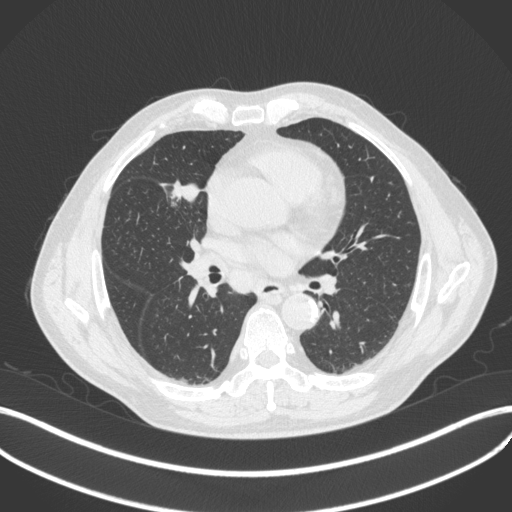
Chest CT, one axial slice; slice 204 of 429 in the series (ordered by position); reconstruction kernel B31f; lung window (W 1500 / L -600 HU); 1 mm slice thickness; 512 × 512 image matrix. Patient: male, 61 years. From the clinical record (not read from this slice): clinical TNM (as recorded): T2b N1 M0.
Outlined on this slice (bounding box drawn by a radiologist):
- lung tumour (recorded histology: squamous cell carcinoma): box from (x=165, y=174) to (x=208, y=200) px